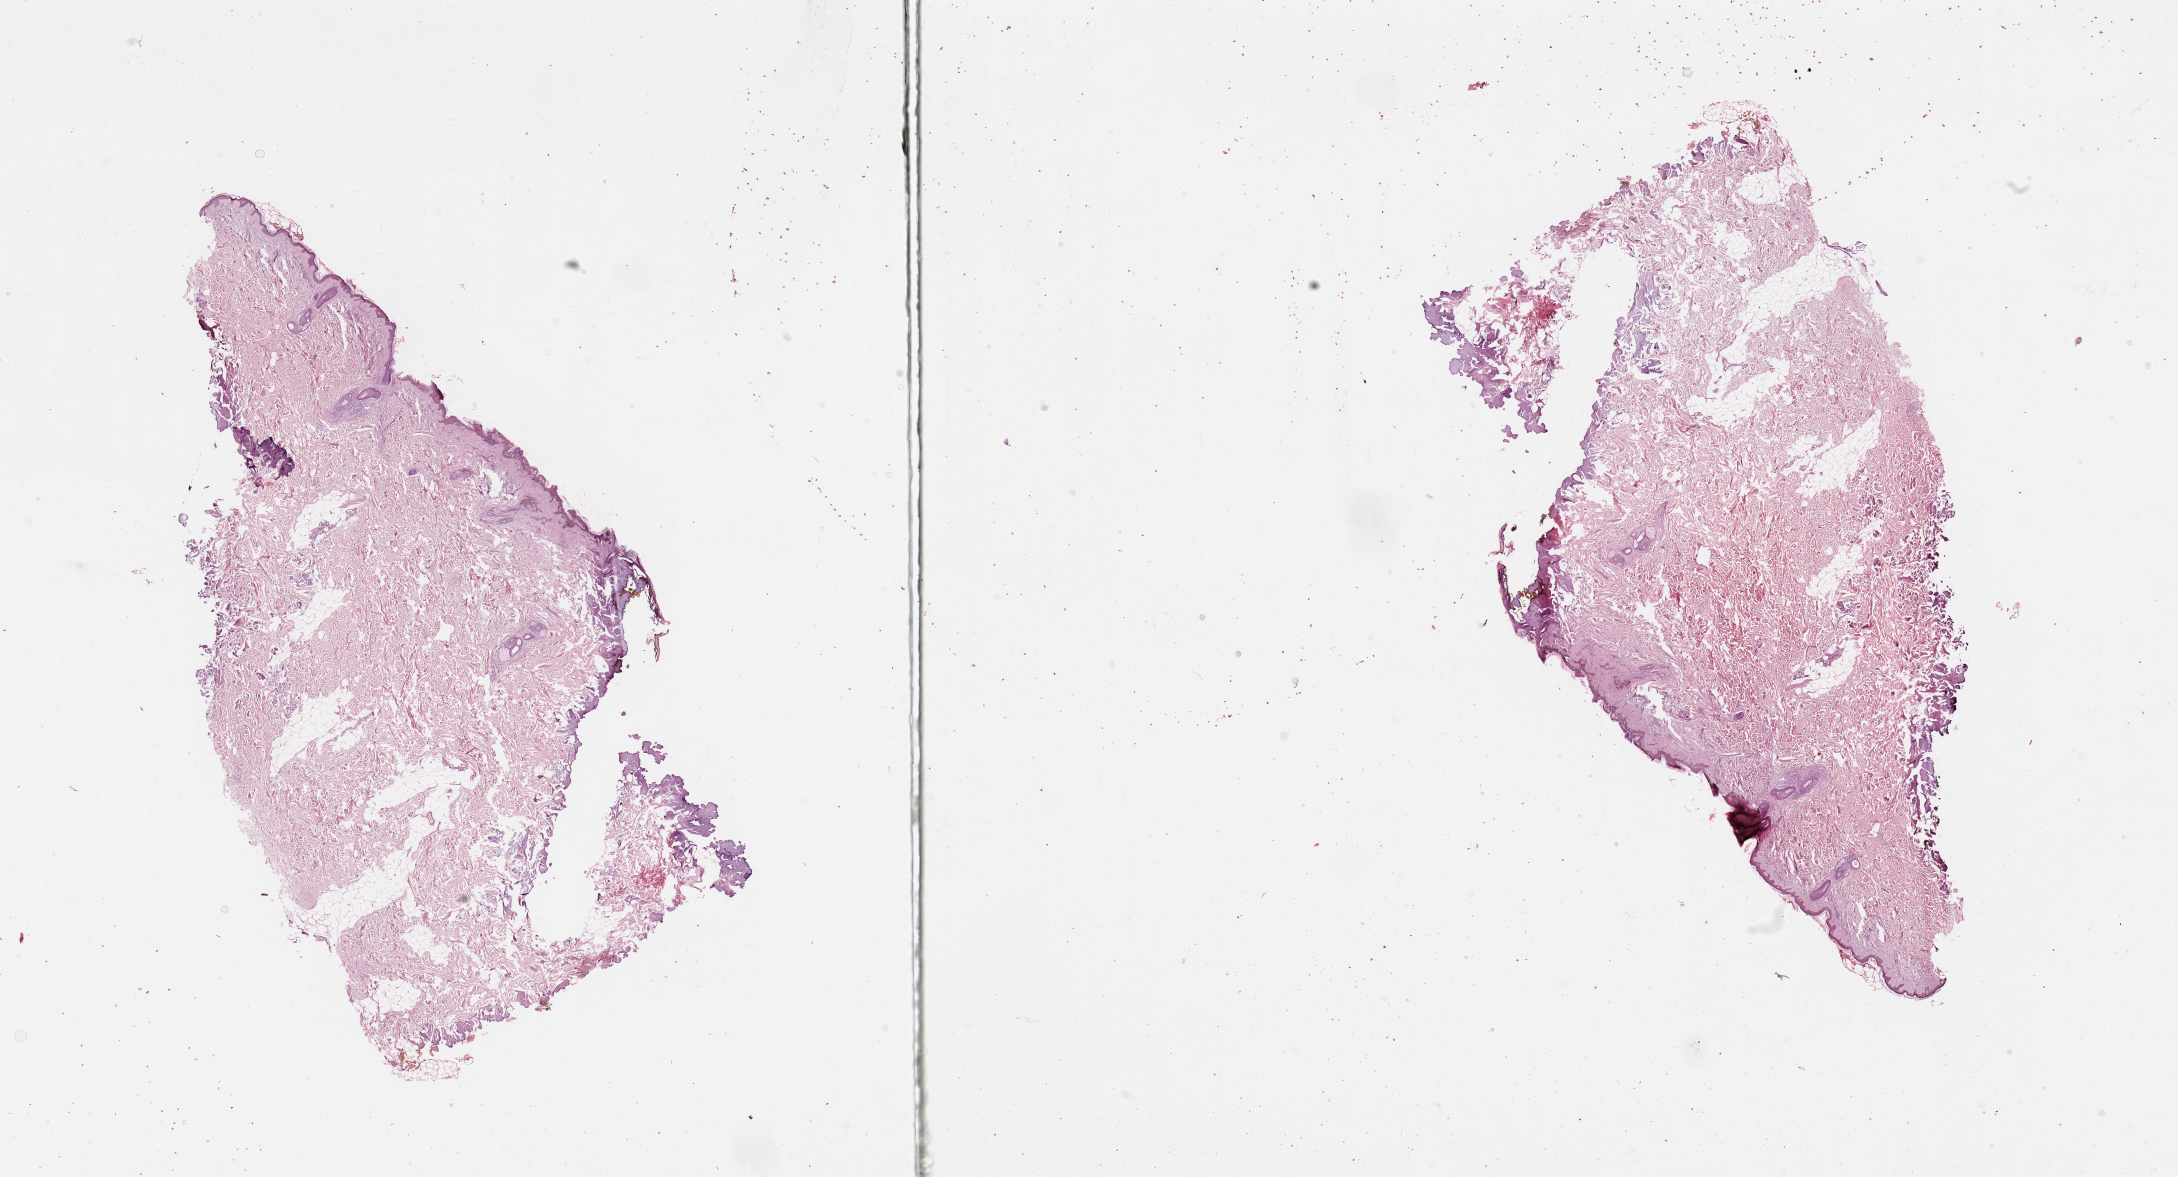
Digitized H&E tissue section (whole slide) — shown as a low-resolution overview of the whole scanned area (about 34.5 x 18.6 mm). Normal (non-tumour) tissue sample, sampled site: trunk. Female, 53 y/o.
This section: normal (non-tumour) tissue from the same patient. Patient diagnosis: Malignant melanoma, NOS.